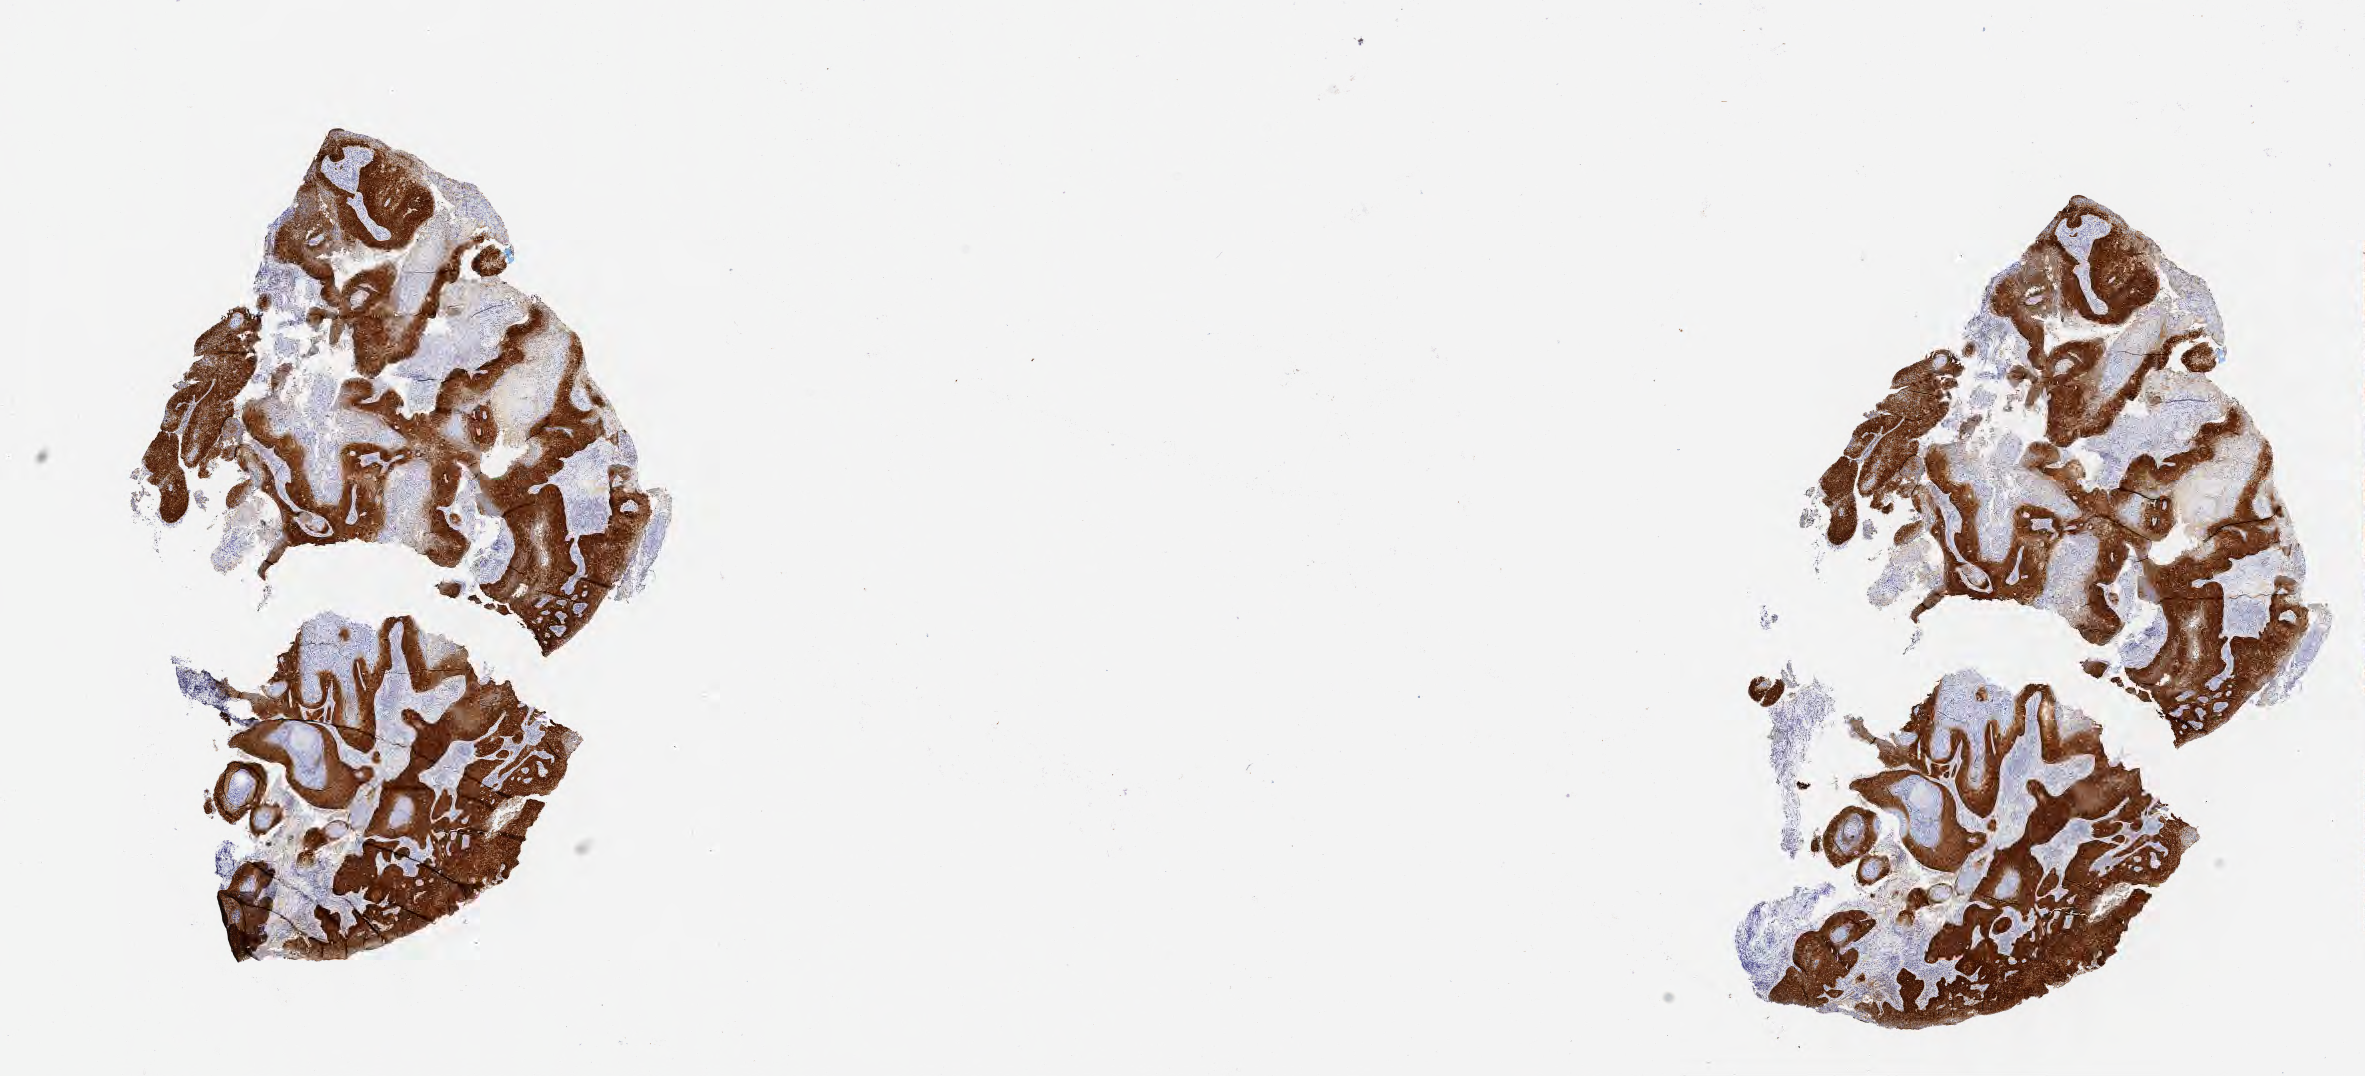
IHC for p16 (p16INK4a), whole-slide image, low-resolution overview of the scanned area, about 19.1 x 8.7 mm. Specimen: tumor tissue. Anatomic site: cervix. Patient female; 32 years old.
Diagnosis: Squamous cell carcinoma, keratinizing, NOS.